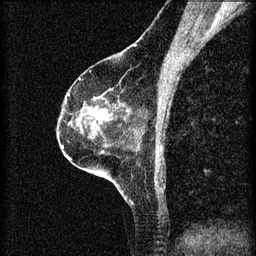
Breast MRI (dynamic contrast-enhanced), one sagittal slice; slice 39 of 60 in the series (ordered by position); 3 images stored at this slice position (order not interpretable as contrast timing); 1.5 T; TE 4.2 ms, TR 8.2 ms; 2 mm slice thickness; 256 × 256 image matrix, field of view 180 × 180 mm. Female patient, age 60 years.
Outlined on this slice (semi-automatically segmented with operator editing):
- analysis volume of interest (the breast-tissue region the enhancement analysis was run in; not a lesion): bounding box <78,96,113,131> (left, top, right, bottom; pixels)
- tumour enhancement mask (voxels above the 70 % enhancement threshold inside the analysis volume of interest): <90,98,112,121>